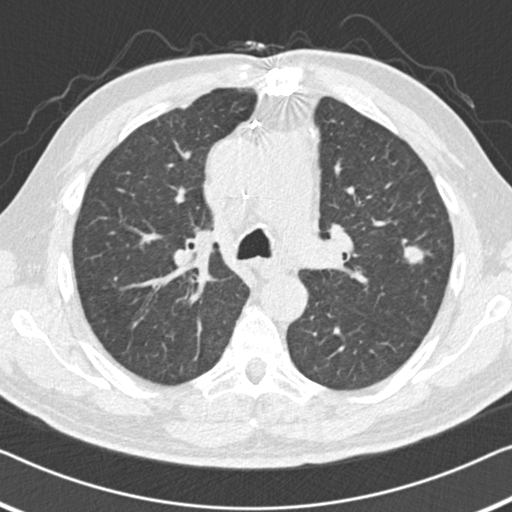
Low-dose screening chest CT, one axial slice. Slice 103 of 155 in the series (ordered by position). 120 kVp. Lung window (W 1500 / L -600 HU). 512 × 512 image matrix.
Outlined on this slice (outlined manually by an expert reader):
- lesion 1 (tumor, upper lobe of left lung): bounding box <403,243,428,265> (left, top, right, bottom; pixels)